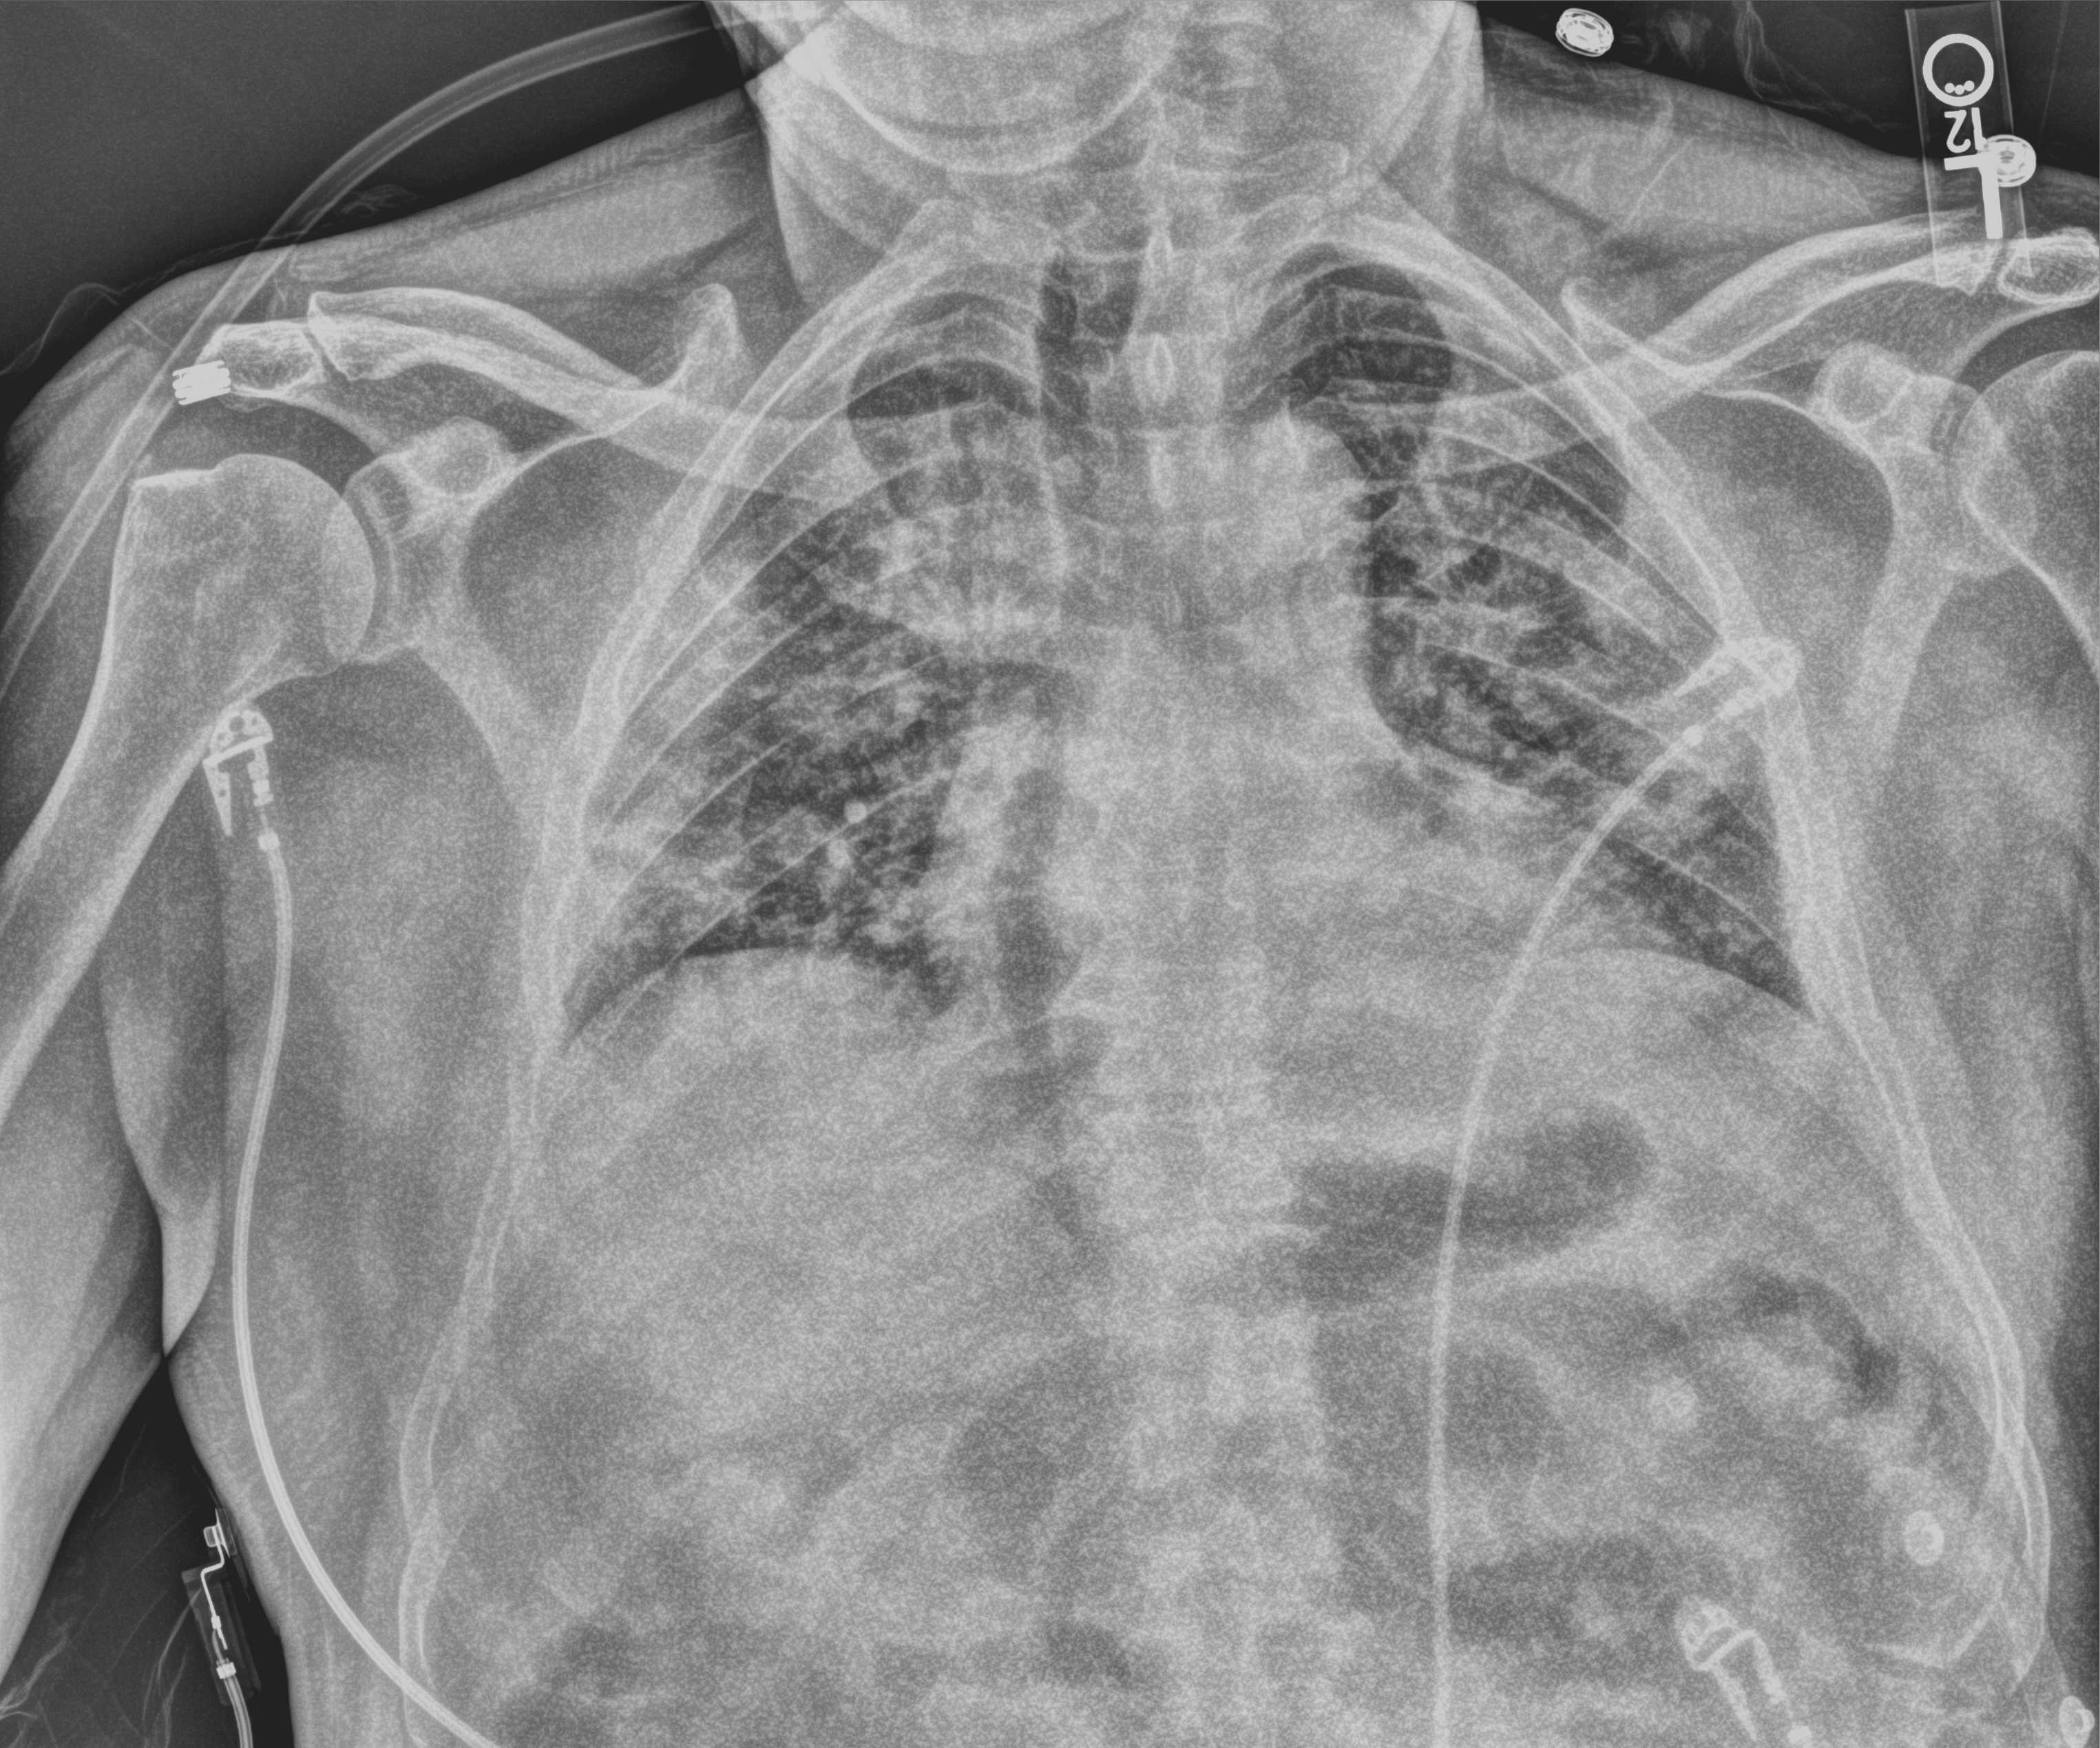
Chest X-ray (portable). Male patient hospitalised with COVID-19, age 60–74 years.
From the hospital-stay record, not from the radiograph (when in the stay this image was taken is not recorded): chronic kidney disease (admission record): no; mechanically ventilated during this hospital stay: no; admitted to intensive care during this hospital stay: no.